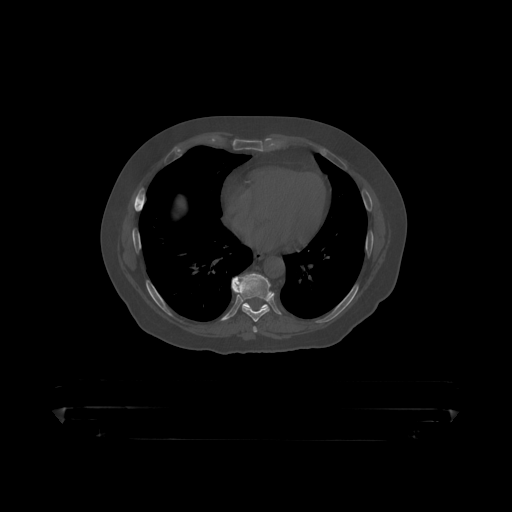
CT including the spine, one axial slice. Slice 253 of 390 in the series (ordered by position). Reconstruction kernel STANDARD. 120 kVp. Bone window (W 1800 / L 400 HU). 1.25 mm slice thickness. 512 × 512 image matrix, field of view 650 × 650 mm. Patient: male, 60 years. Case-level facts recorded for this patient, not image findings: primary cancer: prostate.
Outlined on this slice (semi-automatic segmentation, software-assisted and operator-edited):
- T8 vertebra: bounding box <232,273,272,319> (left, top, right, bottom; pixels)
- T9 vertebra: <232,277,268,309>